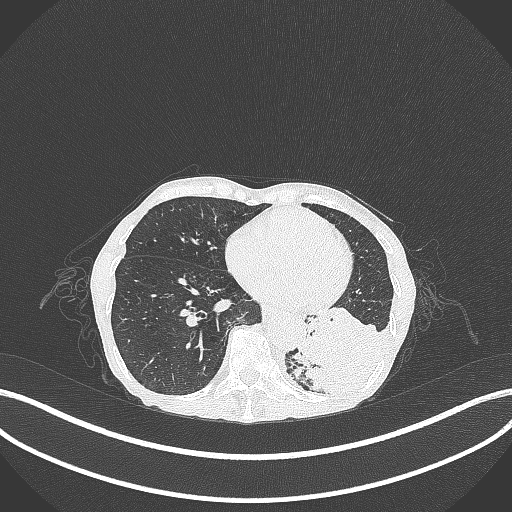
Chest CT, one axial slice; slice 85 of 347 in the series (ordered by position); reconstruction kernel B70f; 120 kVp; lung window (W 1500 / L -600 HU); 1 mm slice thickness; 512 × 512 image matrix. Female patient, age 70 years. Case-level facts recorded for this patient, not image findings: clinical TNM (as recorded): T3 N0 M0; histopathological grade: G3.
Outlined on this slice (bounding box drawn by a radiologist):
- lung tumour (recorded histology: small cell carcinoma): bounding box [x1, y1, x2, y2] px = [289, 314, 381, 400]